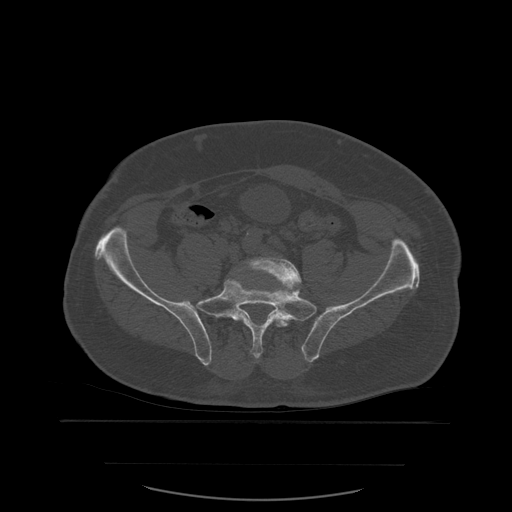
CT including the spine, one axial slice; slice 122 of 590 in the series (ordered by position); bone window (W 1800 / L 400 HU); 1.25 mm slice thickness; 512 × 512 image matrix, field of view 479 × 479 mm. Patient age 71 years. Case-level facts recorded for this patient, not image findings: primary cancer: lung; vertebrae with lytic lesions (as recorded): T1, T2, L5, S1.
Outlined on this slice (semi-automatically segmented with operator editing):
- L5 vertebra: bounding box (x1, y1, x2, y2) in pixels: (221, 257, 302, 356)